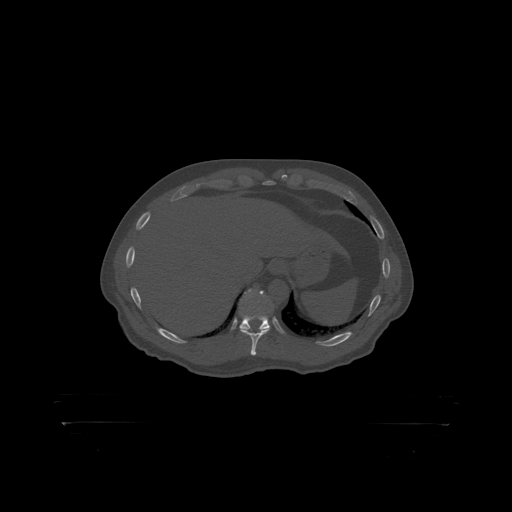
CT including the spine, one axial slice; reconstruction kernel STANDARD; 120 kVp; bone window (W 1800 / L 400 HU); 512 × 512 image matrix. Patient: male, 46 years. From the clinical record (not read from this slice): primary cancer: skin.
Annotated regions visible in this slice (semi-automatically segmented with operator editing):
- T11 vertebra: box from (x=240, y=290) to (x=273, y=319) px